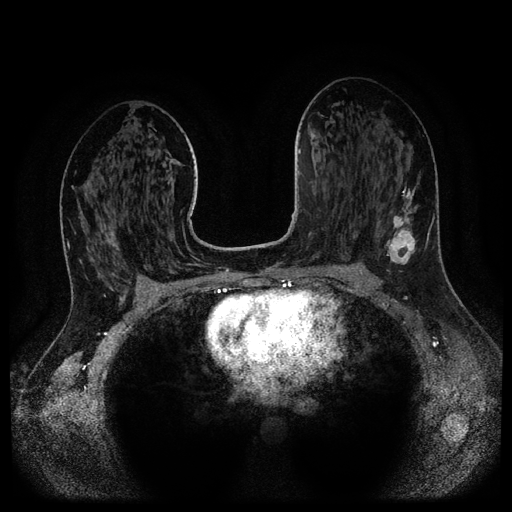
Breast MRI (dynamic contrast-enhanced, multi-phase), one axial slice. Slice 62 of 116 in the series (ordered by position). Dynamic contrast-enhanced series, time point 2 of 5 at this slice position (early post-contrast). 1.5 T. TE 2.6 ms, TR 5.3 ms. 2.1 mm slice thickness. 512 × 512 image matrix, field of view 360 × 360 mm. Female patient, age 37 years.
Annotated regions visible in this slice (semi-automatic segmentation, software-assisted and operator-edited):
- breast lesion (labelled 'tumour' in the annotation; benign lesions carry a separate 'benign' label): bounding box [x1, y1, x2, y2] px = [384, 183, 418, 272]